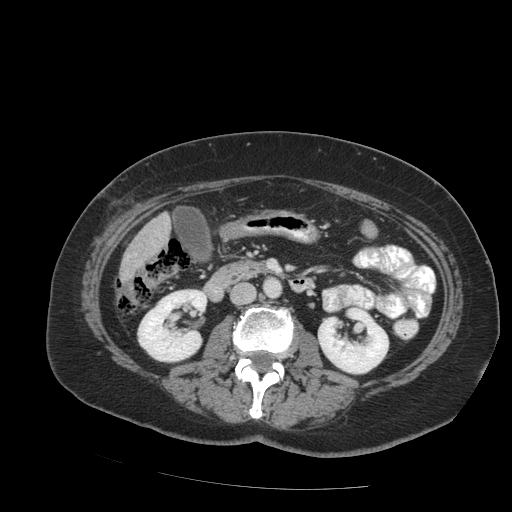
Contrast-enhanced abdominal CT (liver protocol), one axial slice. Position 25 of 99 along the scan axis. 140 kVp. Soft-tissue window (W 400 / L 40 HU). 2.5 mm slice thickness. 512 × 512 image matrix, field of view 400 × 400 mm. From the clinical record (not read from this slice): diagnosis: hepatocellular carcinoma (patient treated with transarterial chemoembolisation; whether this scan precedes or follows treatment is not stated here); TNM stage (as recorded): Stage-IVB; Child-Pugh class: A; tumour differentiation: moderately differentiated.
Structures marked on this image (semi-automatic segmentation, software-assisted and operator-edited):
- liver parenchyma outside the tumour (the mass and vessels are separate outlines, so this box may not span the whole liver): bounding box <120,212,170,282> (left, top, right, bottom; pixels)